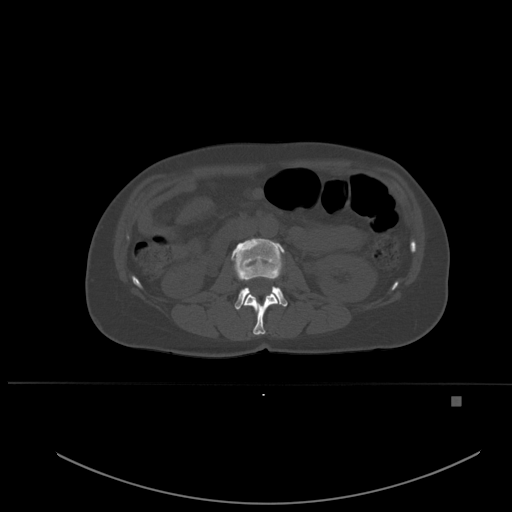
CT including the spine, one axial slice; slice 222 of 651 in the series (ordered by position); bone window (W 1800 / L 400 HU); 1.5 mm slice thickness; 512 × 512 image matrix. Female patient, age 49 years. Case-level facts recorded for this patient, not image findings: primary cancer: breast; vertebrae with lytic lesions (as recorded): L3, T12, L4.
Annotated regions visible in this slice (semi-automatic segmentation, software-assisted and operator-edited):
- L1 vertebra: bounding box (x1, y1, x2, y2) in pixels: (244, 293, 278, 335)
- L2 vertebra: (231, 238, 288, 310)